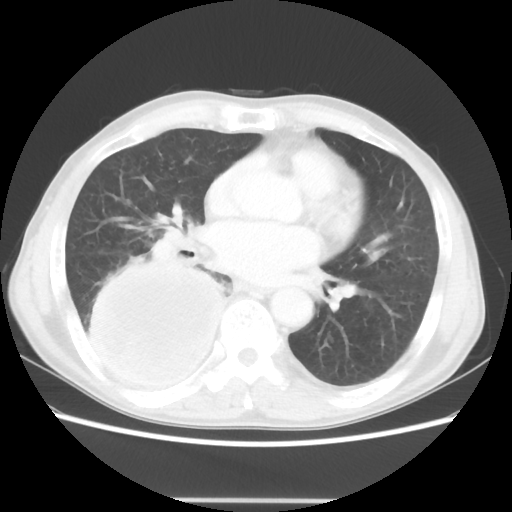
Chest CT, one axial slice. Position 21 of 48 along the scan axis. 100 kVp. Lung window (W 1500 / L -600 HU). 5 mm slice thickness. 512 × 512 image matrix, field of view 361 × 361 mm. Male patient, age 66 years. Case-level facts recorded for this patient, not image findings: clinical TNM (as recorded): T4 N1 M1.
Structures marked on this image (rectangle marked by the reading radiologist):
- lung tumour (recorded histology: small cell carcinoma): bounding box (x1, y1, x2, y2) in pixels: (84, 250, 231, 394)